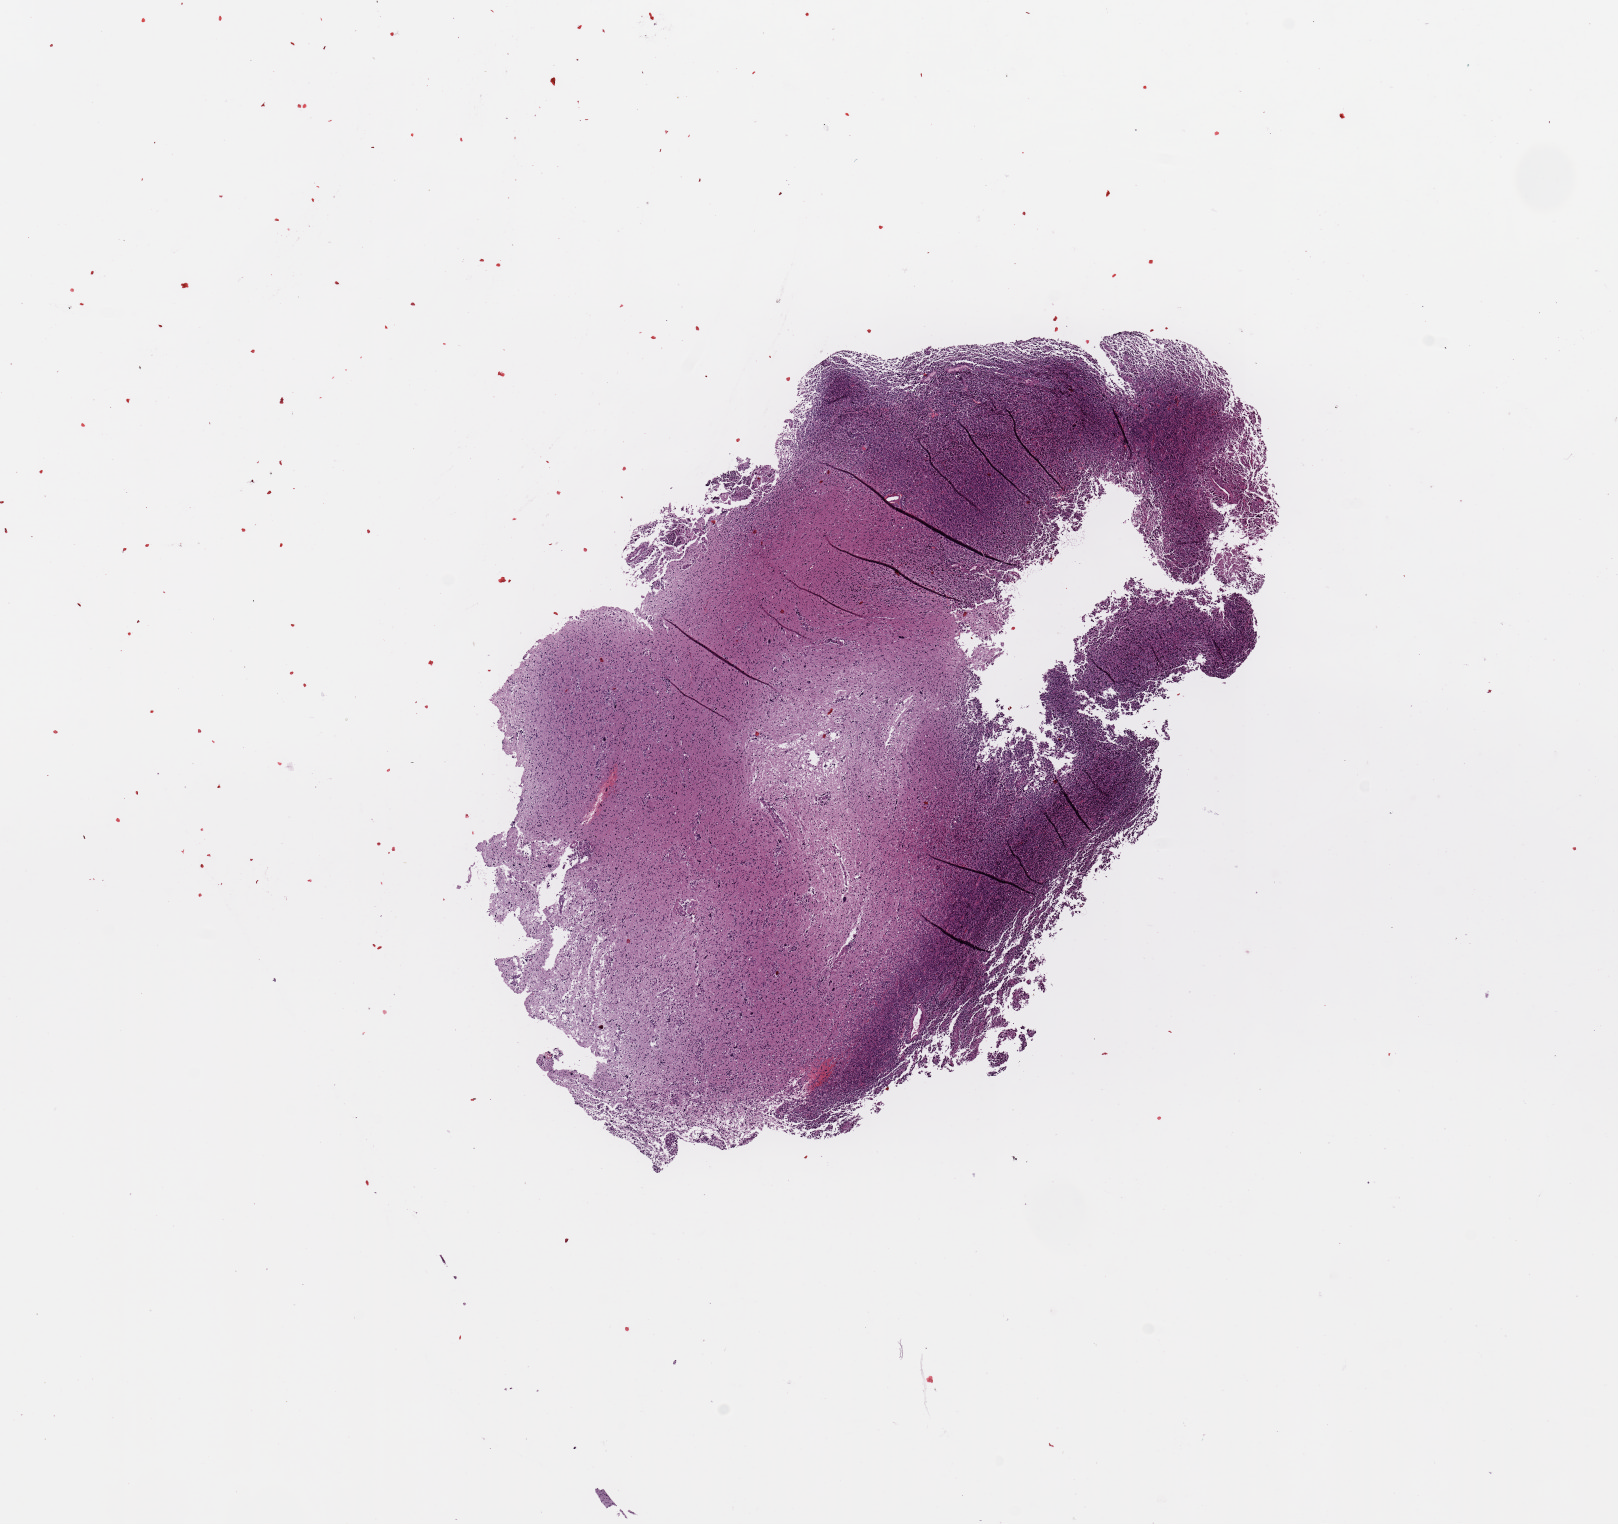
Whole-slide histology image, Hematoxylin and eosin (H&E) stained — low-resolution overview of the scanned area, about 12.8 x 12.1 mm (slide scanned at 20x); brain, tumour tissue. 39-year-old female patient.
- histologic diagnosis: Glioblastoma